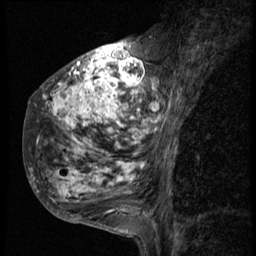
Breast MRI (dynamic contrast-enhanced), one sagittal slice. Position 20 of 58 along the scan axis. 3 images stored at this slice position (order not interpretable as contrast timing). 1.5 T. TE 4.2 ms, TR 9 ms. 256 × 256 image matrix, field of view 180 × 180 mm. Patient: female, 50 years. From the clinical record (not read from this slice): setting: breast cancer imaged before/during neoadjuvant chemotherapy; receptor status: triple-negative.
Annotated regions visible in this slice (semi-automatically segmented with operator editing):
- analysis volume of interest (the breast-tissue region the enhancement analysis was run in; not a lesion): box from (x=24, y=48) to (x=185, y=214) px
- tumour enhancement mask (voxels above the 140 % enhancement threshold inside the analysis volume of interest): (x=30, y=48)–(x=181, y=202)